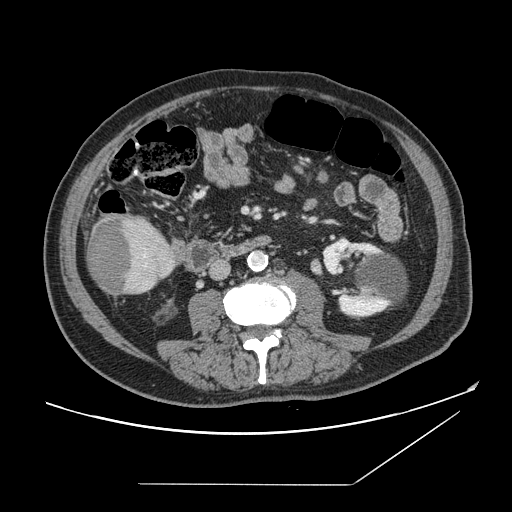
Contrast-enhanced abdominal CT, one axial slice. Slice 38 of 166 in the series (ordered by position). Intravenous contrast given. Soft-tissue window (W 400 / L 40 HU). 2.5 mm slice thickness. 512 × 512 image matrix, field of view 416 × 416 mm. Male patient, age 80 years. From the clinical record (not read from this slice): diagnosis: colorectal cancer liver metastases, imaged before liver resection; multiple liver metastases: no; largest metastasis: 2.2 cm; chemotherapy before resection: no.
Annotated regions visible in this slice (outlined manually by an expert reader):
- liver: bounding box (x1, y1, x2, y2) in pixels: (88, 213, 176, 295)
- liver metastasis: (90, 219, 134, 293)